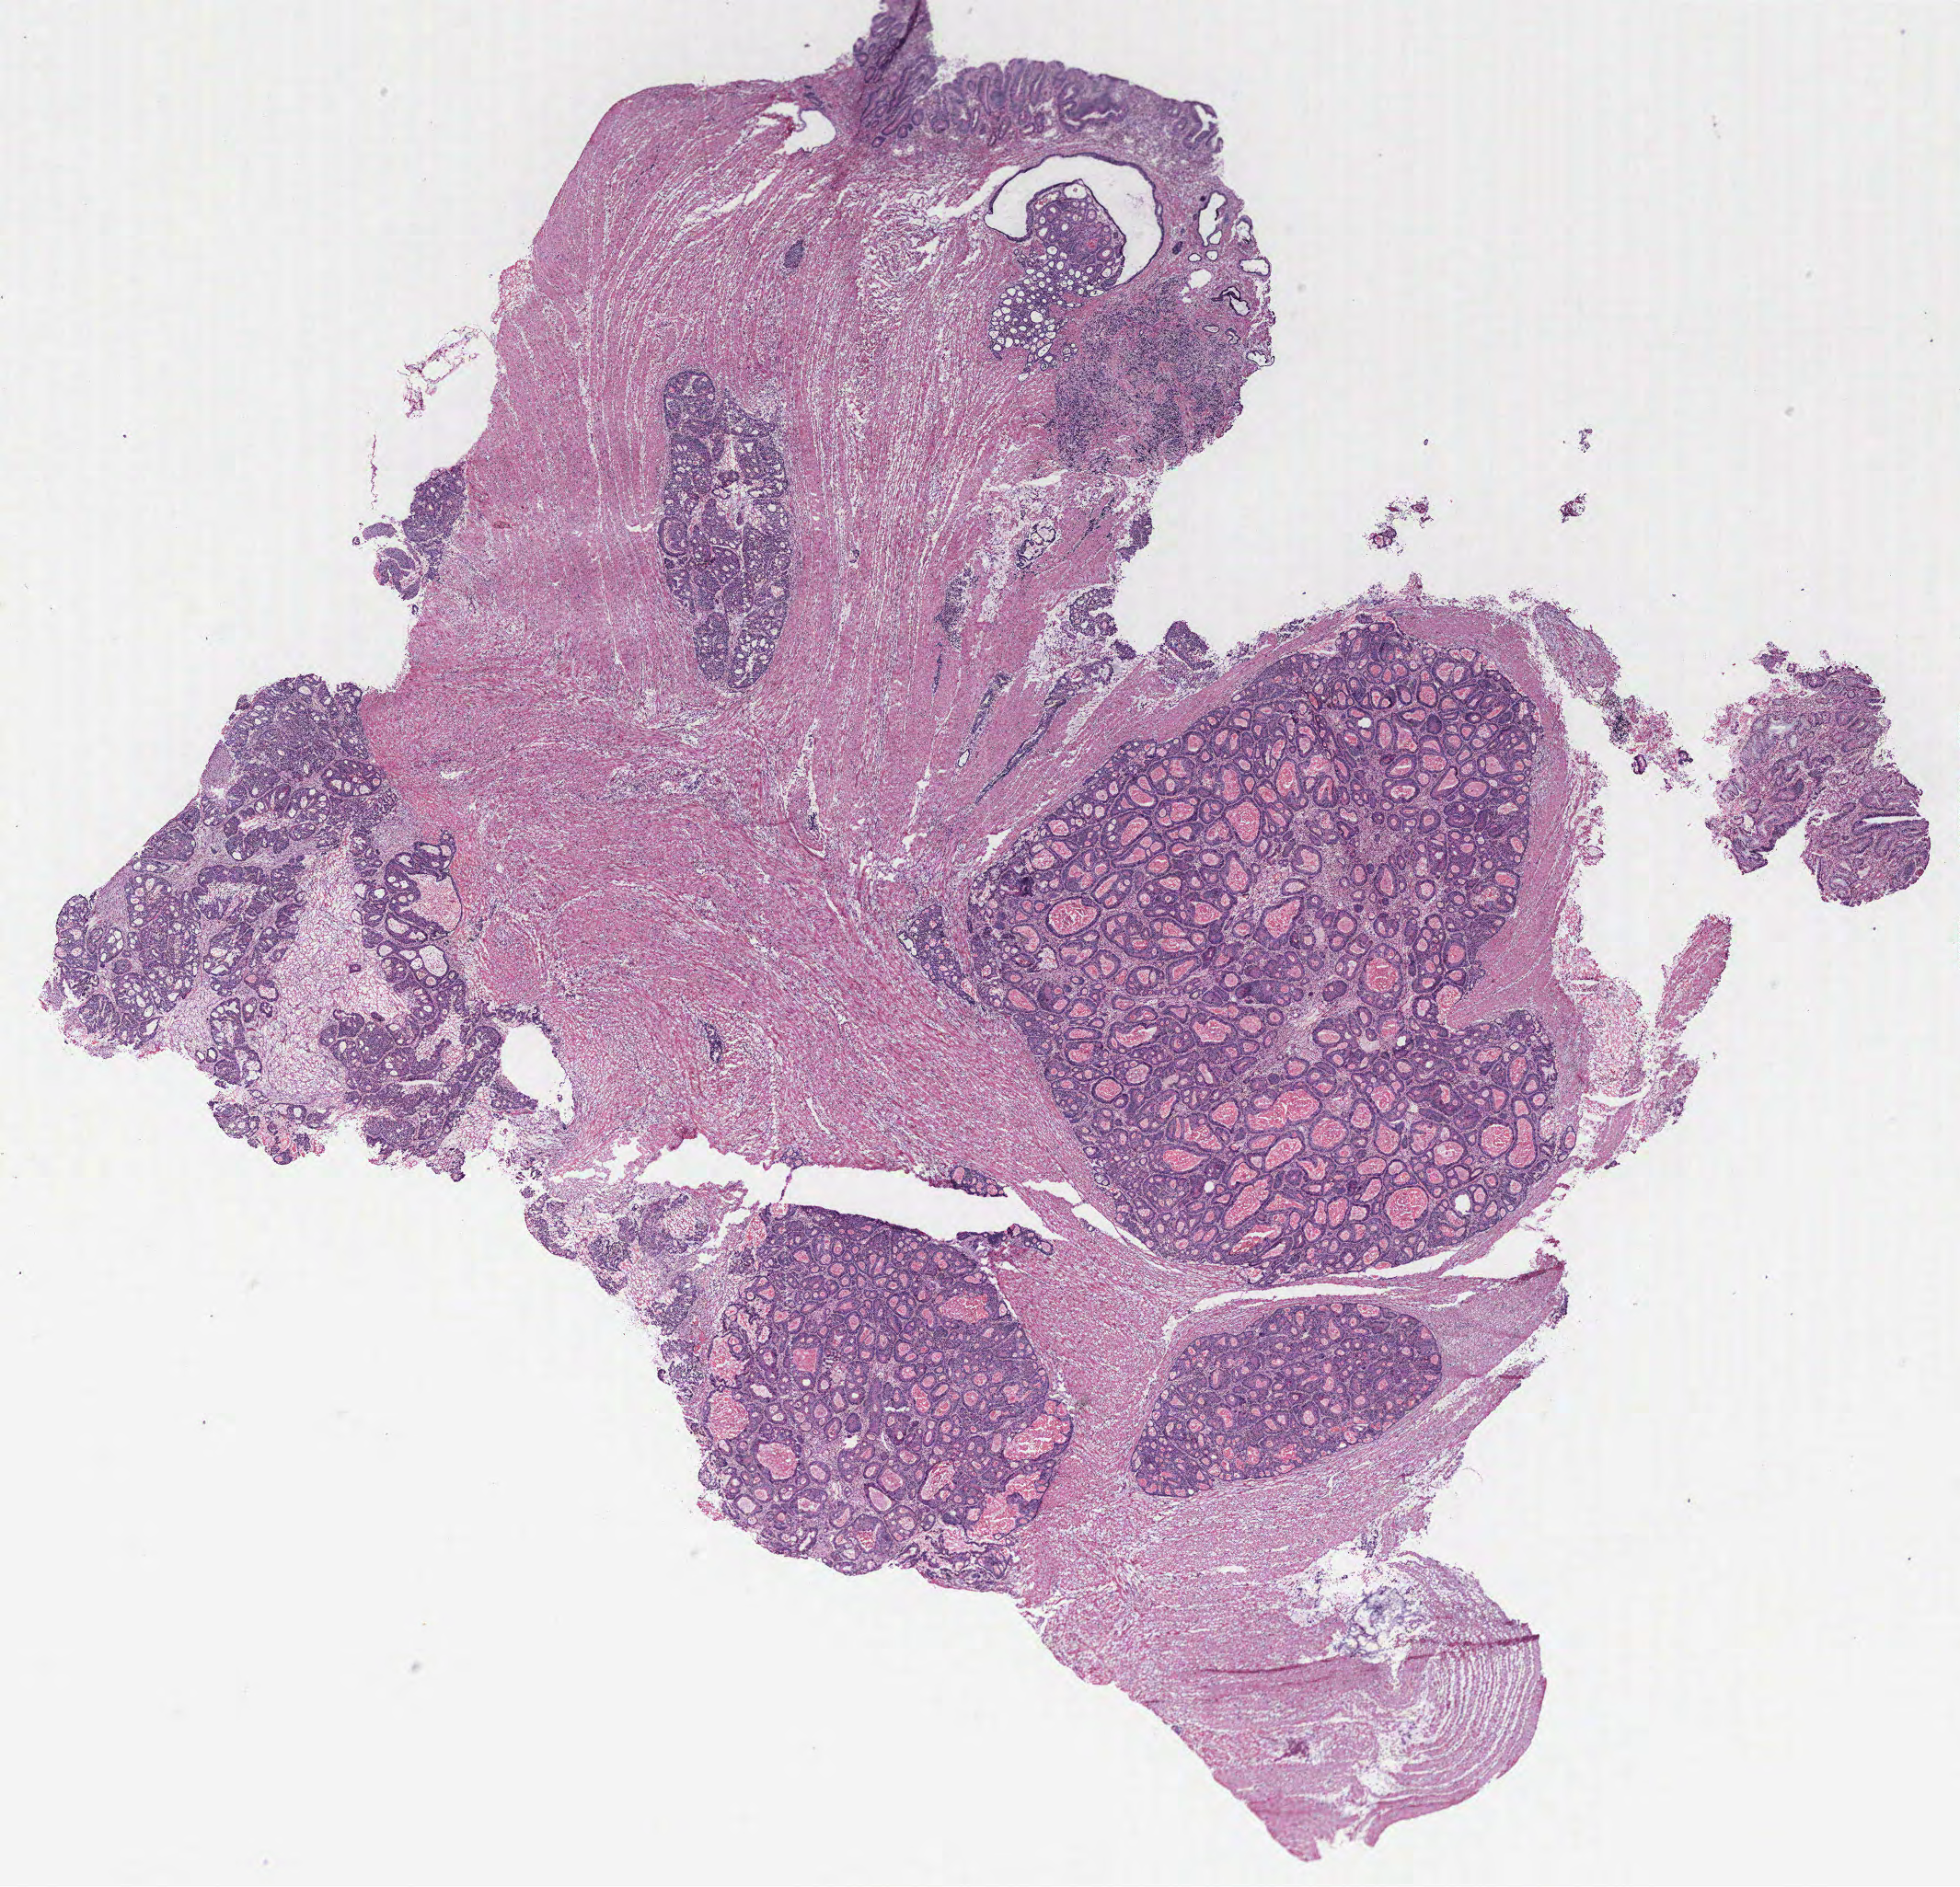
Whole-slide histology image, H&E-stained, shown as a low-resolution overview of the whole scanned area (about 17.0 x 16.4 mm, from a 40x scan); tumour tissue sample, colon. 67-year-old male patient.
* AJCC pathologic stage: IIIB
* primary tumour site (as recorded): colon
* histologic diagnosis: Adenocarcinoma, NOS